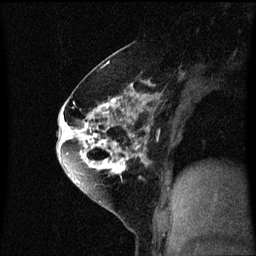
Breast MRI (dynamic contrast-enhanced), one sagittal slice. Slice 34 of 60 in the series (ordered by position). Dynamic contrast-enhanced series, image 2 of 3 at this slice position (ordered by acquisition). 1.5 T. TE 4.2 ms, TR 8.4 ms. 2 mm slice thickness. 256 × 256 image matrix. Female patient, age 60 years.
Structures marked on this image (semi-automatically segmented with operator editing):
- analysis volume of interest (the breast-tissue region the enhancement analysis was run in; not a lesion): box from (x=64, y=70) to (x=147, y=195) px
- tumour enhancement mask (voxels above the 70 % enhancement threshold inside the analysis volume of interest): (x=64, y=70)–(x=147, y=187)